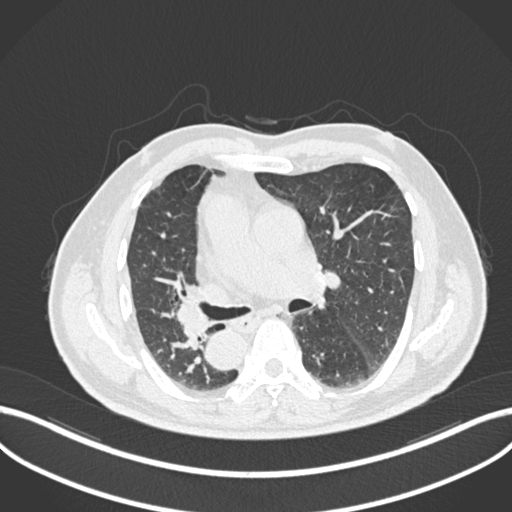
Chest CT, one axial slice. Slice 125 of 206 in the series (ordered by position). Lung window (W 1500 / L -600 HU). 512 × 512 image matrix, field of view 400 × 400 mm. Male patient, age 67 years. From the clinical record (not read from this slice): clinical TNM (as recorded): T2a N0 M0.
Outlined on this slice (bounding box drawn by a radiologist):
- lung tumour (recorded histology: squamous cell carcinoma): box from (x=176, y=293) to (x=214, y=350) px